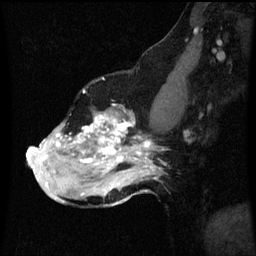
Breast MRI (dynamic contrast-enhanced), one sagittal slice; slice 37 of 60 in the series (ordered by position); dynamic contrast-enhanced series, image 2 of 3 at this slice position (ordered by acquisition); 1.5 T; TE 4.2 ms, TR 8.9 ms; 2 mm slice thickness; 256 × 256 image matrix, field of view 200 × 200 mm. Female patient, age 49 years. From the clinical record (not read from this slice): setting: breast cancer imaged before/during neoadjuvant chemotherapy; receptor status: HR-positive, HER2-negative.
Outlined on this slice (semi-automatic segmentation, software-assisted and operator-edited):
- analysis volume of interest (the breast-tissue region the enhancement analysis was run in; not a lesion): bounding box [x1, y1, x2, y2] px = [28, 106, 159, 199]
- tumour enhancement mask (voxels above the 70 % enhancement threshold inside the analysis volume of interest): [28, 114, 155, 187]